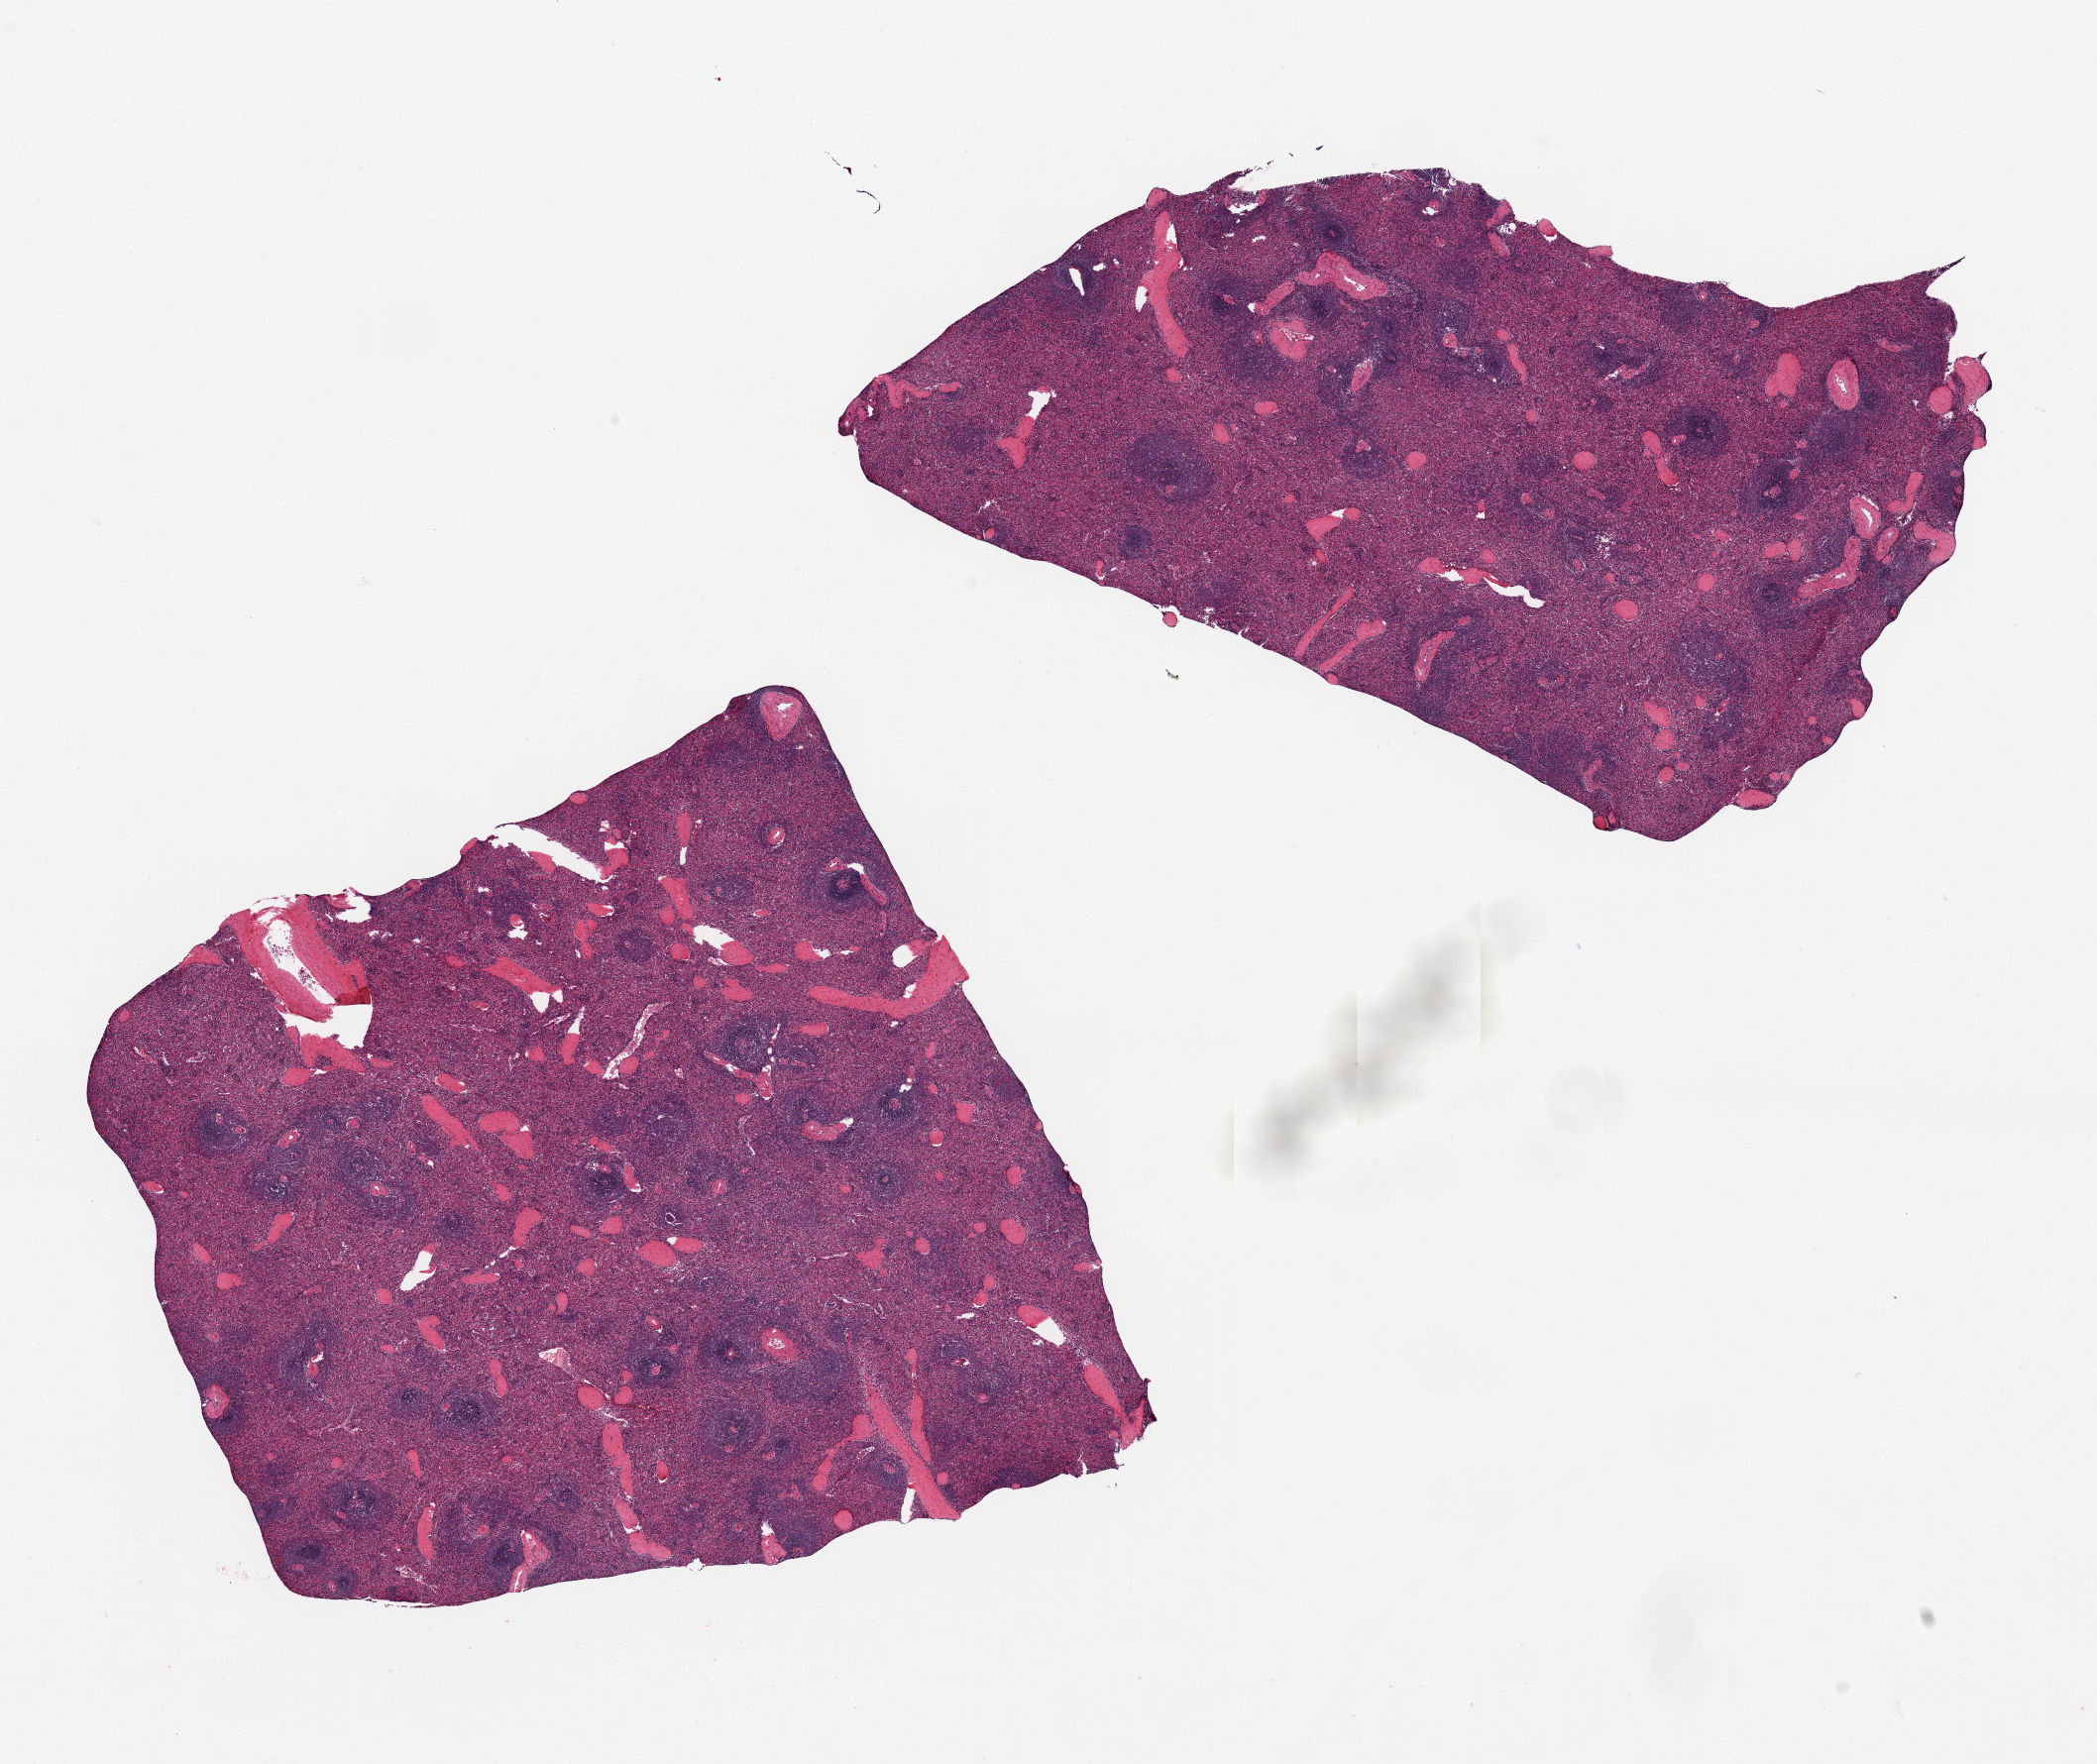
Haematoxylin and eosin whole-slide image, shown as a low-resolution overview of the whole scanned area (about 16.7 x 14.1 mm); PAXgene-fixed, paraffin-embedded tissue; section of spleen (target tissue); donor tissue sample. Donor: male.
Reviewer comment on this tissue sample: 2 aliquots, ~7x6mm.